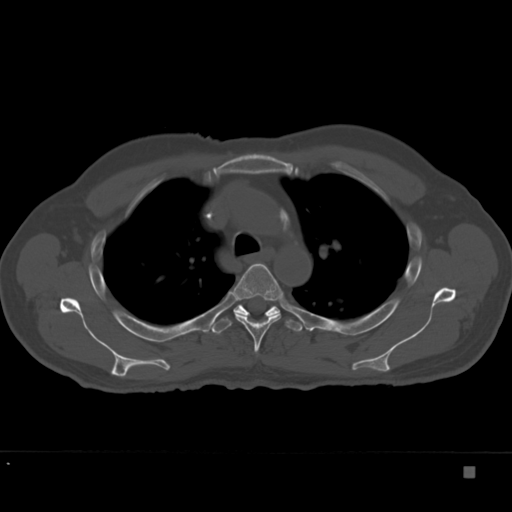
CT including the spine, one axial slice. Slice 266 of 332 in the series (ordered by position). Bone window (W 1800 / L 400 HU). 512 × 512 image matrix, field of view 389 × 389 mm. Patient: male, 72 years. Case-level facts recorded for this patient, not image findings: primary cancer: skeletal.
Outlined on this slice (semi-automatic segmentation, software-assisted and operator-edited):
- T4 vertebra: bounding box (x1, y1, x2, y2) in pixels: (232, 263, 283, 354)
- T5 vertebra: (211, 304, 302, 334)